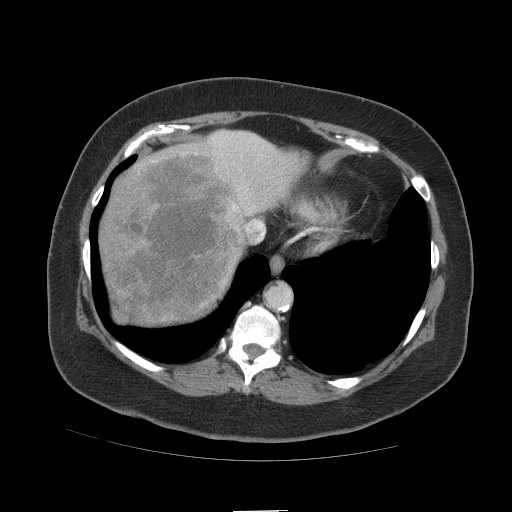
Contrast-enhanced abdominal CT (liver protocol), one axial slice. Position 91 of 109 along the scan axis. Reconstruction kernel STANDARD. Soft-tissue window (W 400 / L 40 HU). 2.5 mm slice thickness. 512 × 512 image matrix, field of view 420 × 420 mm. From the clinical record (not read from this slice): diagnosis: hepatocellular carcinoma (patient treated with transarterial chemoembolisation; whether this scan precedes or follows treatment is not stated here); TNM stage (as recorded): Stage-IVB; Child-Pugh class: A; tumour nodularity: multinodular.
Structures marked on this image (semi-automatic segmentation, software-assisted and operator-edited):
- liver parenchyma outside the tumour (the mass and vessels are separate outlines, so this box may not span the whole liver): box from (x=98, y=130) to (x=306, y=324) px
- mass: (x=100, y=145)–(x=246, y=321)
- liver vessels: (x=213, y=133)–(x=258, y=209)